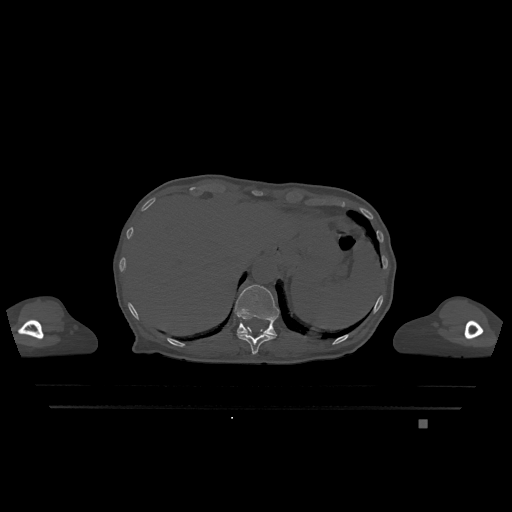
CT including the spine, one axial slice; bone window (W 1800 / L 400 HU); 0.5 mm slice thickness; 512 × 512 image matrix, field of view 500 × 500 mm. Patient: female, 74 years. Case-level facts recorded for this patient, not image findings: primary cancer: lung; vertebrae with lytic lesions (as recorded): T1, T4, T5, T6, L4, L5.
Outlined on this slice (semi-automatic segmentation, software-assisted and operator-edited):
- T11 vertebra: bounding box [x1, y1, x2, y2] px = [237, 327, 276, 354]
- T12 vertebra: [234, 285, 279, 336]